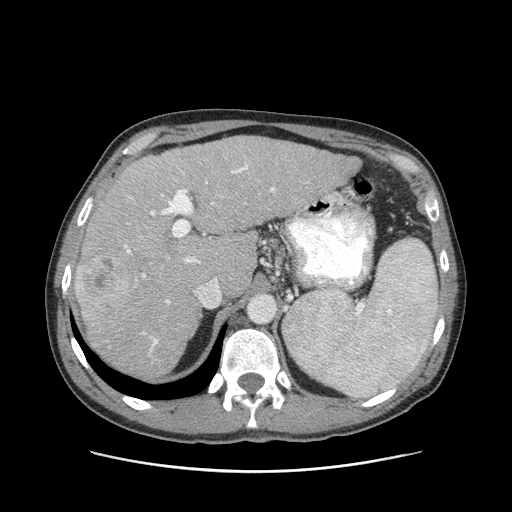
Contrast-enhanced abdominal CT (liver protocol), one axial slice. Reconstruction kernel STANDARD. 120 kVp. Soft-tissue window (W 400 / L 40 HU). 2.5 mm slice thickness. 512 × 512 image matrix, field of view 380 × 380 mm. Case-level facts recorded for this patient, not image findings: diagnosis: hepatocellular carcinoma (patient treated with transarterial chemoembolisation; whether this scan precedes or follows treatment is not stated here); TNM stage (as recorded): Stage-II; Child-Pugh class: A; tumour differentiation: moderately differentiated; tumour size: 1 cm.
Annotated regions visible in this slice (semi-automatic segmentation, software-assisted and operator-edited):
- liver parenchyma outside the tumour (the mass and vessels are separate outlines, so this box may not span the whole liver): bounding box [x1, y1, x2, y2] px = [74, 136, 360, 378]
- mass: [77, 250, 134, 314]
- liver vessels: [124, 164, 275, 351]